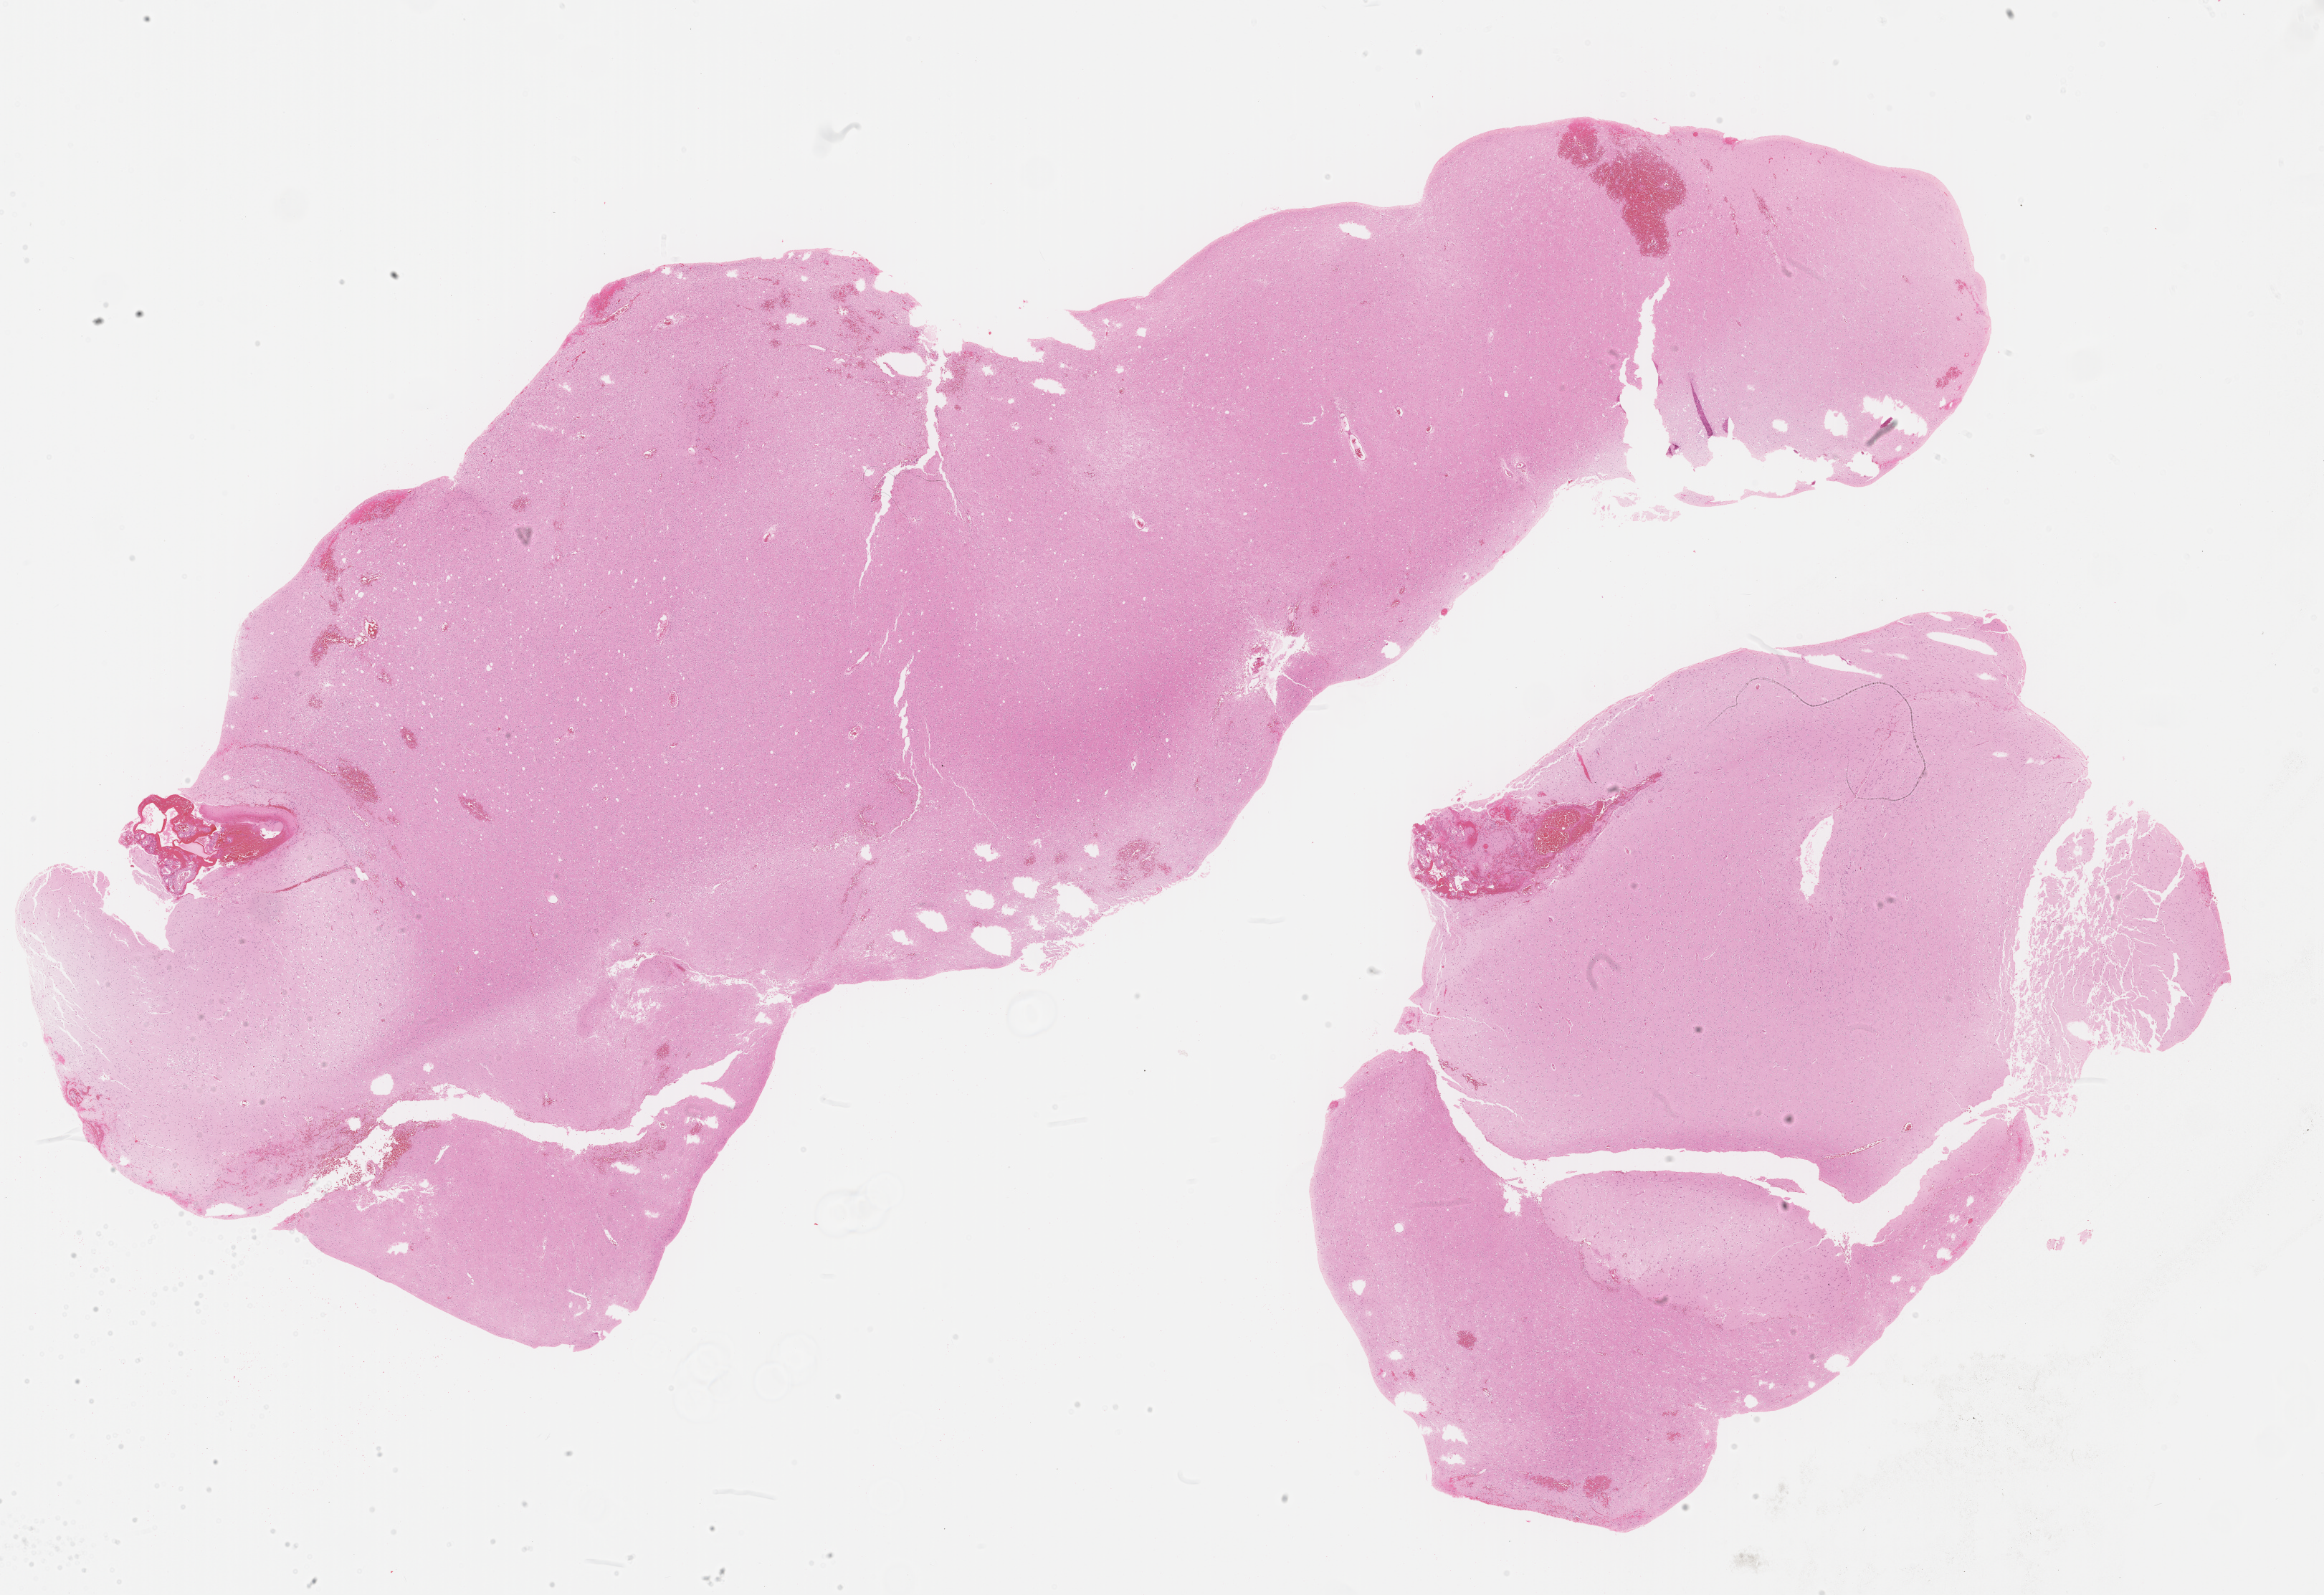
Digitized Hematoxylin and eosin (H&E) stained tissue section (whole slide) — low-resolution overview of the scanned area, about 26.1 x 17.9 mm (from a 40x scan). FFPE section. Sample: primary tumour, brain. Male patient; age at initial diagnosis 40 years. Histologic grade: G2 (moderately differentiated).
- diagnosis: Oligodendroglioma, NOS (cerebrum)